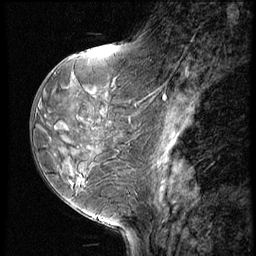
Breast MRI (dynamic contrast-enhanced), one sagittal slice. Slice 26 of 60 in the series (ordered by position). 3 images stored at this slice position (order not interpretable as contrast timing). 1.5 T. TE 4.2 ms, TR 8.9 ms. 2.5 mm slice thickness. 256 × 256 image matrix. Patient: female, 50 years. From the clinical record (not read from this slice): setting: breast cancer imaged before/during neoadjuvant chemotherapy; receptor status: HR-positive, HER2-negative.
Annotated regions visible in this slice (semi-automatic segmentation, software-assisted and operator-edited):
- analysis volume of interest (the breast-tissue region the enhancement analysis was run in; not a lesion): bounding box <38,102,118,213> (left, top, right, bottom; pixels)
- tumour enhancement mask (voxels above the 140 % enhancement threshold inside the analysis volume of interest): <78,178,82,183>